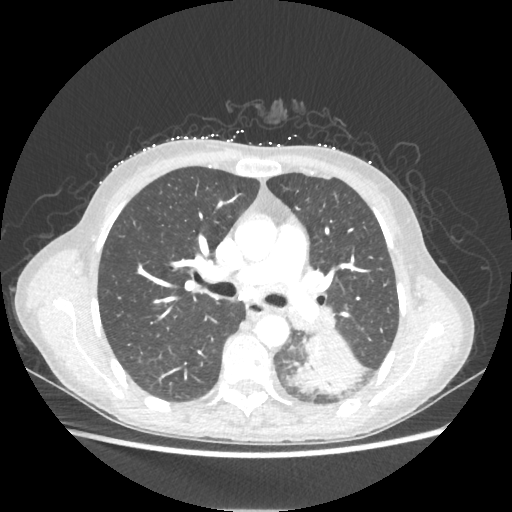
Chest CT, one axial slice. Slice 133 of 221 in the series (ordered by position). 80 kVp. Lung window (W 1500 / L -600 HU). 1.25 mm slice thickness. 512 × 512 image matrix, field of view 360 × 360 mm. Patient: female, 53 years. Case-level facts recorded for this patient, not image findings: clinical TNM (as recorded): T3 N0 M0.
Structures marked on this image (rectangle marked by the reading radiologist):
- lung tumour (recorded histology: adenocarcinoma): bounding box (x1, y1, x2, y2) in pixels: (292, 328, 362, 395)